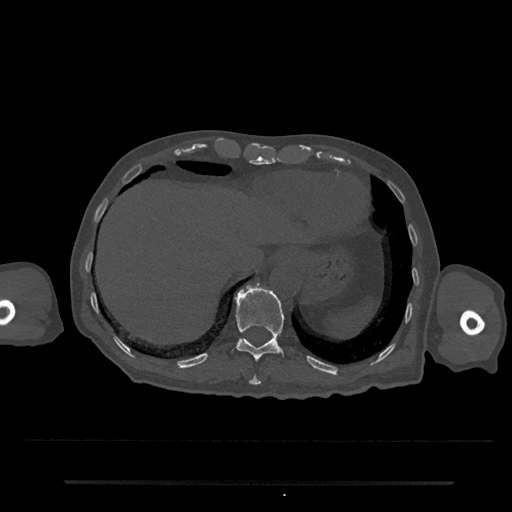
CT including the spine, one axial slice. Slice 255 of 797 in the series (ordered by position). Bone window (W 1800 / L 400 HU). 0.5 mm slice thickness. 512 × 512 image matrix. Patient: male, 74 years. Case-level facts recorded for this patient, not image findings: primary cancer: prostate.
Outlined on this slice (semi-automatic segmentation, software-assisted and operator-edited):
- T10 vertebra: box from (x=249, y=375) to (x=261, y=385) px
- T11 vertebra: (x=234, y=283)–(x=285, y=362)